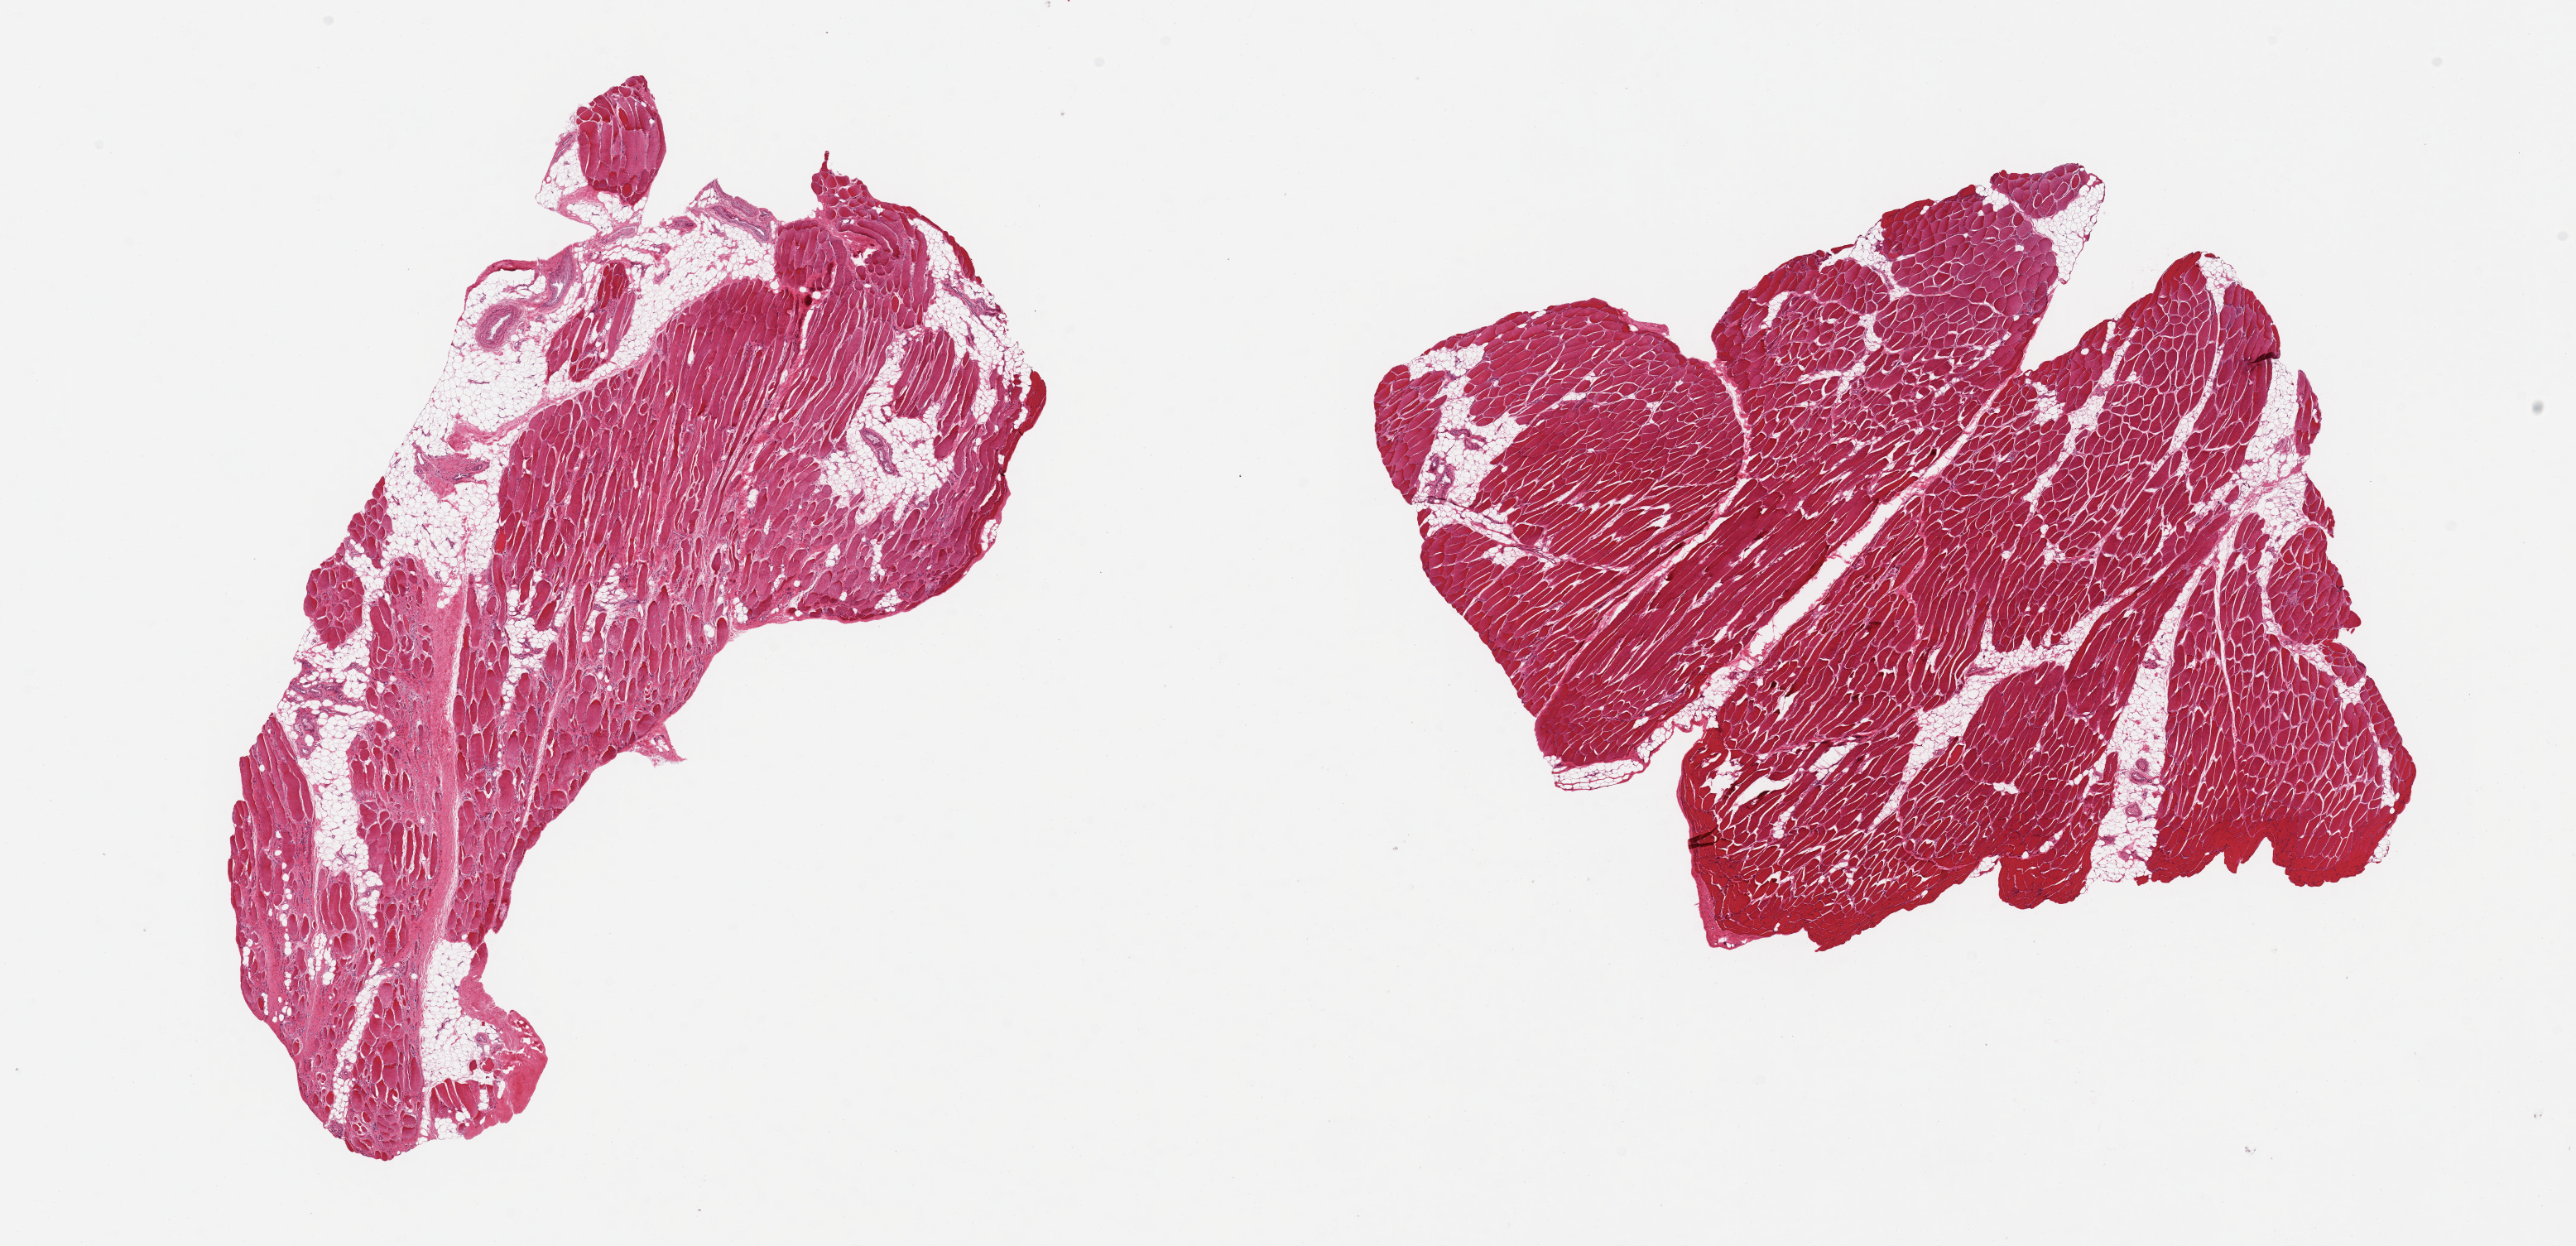
Digitized haematoxylin and eosin-stained section — low-resolution overview of the scanned area, about 24.6 x 11.9 mm; PAXgene-fixed, paraffin-embedded tissue; section of skeletal muscle (target tissue); tissue donor sample. Donor sex: male.
• reviewer comment on this tissue sample: 2 pieces, ~15% interstitial fat/vascular elements